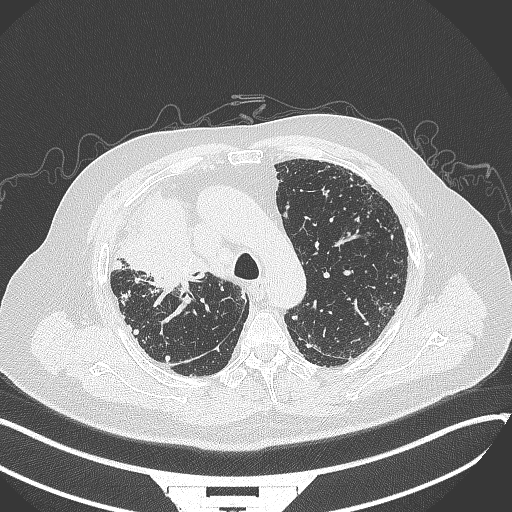
Chest CT, one axial slice; position 258 of 384 along the scan axis; 120 kVp; lung window (W 1500 / L -600 HU); 1 mm slice thickness; 512 × 512 image matrix. Male patient, age 69 years. Case-level facts recorded for this patient, not image findings: clinical TNM (as recorded): T4 N3 M1.
Annotated regions visible in this slice (bounding box drawn by a radiologist):
- lung tumour (recorded histology: adenocarcinoma): bounding box <113,194,215,304> (left, top, right, bottom; pixels)